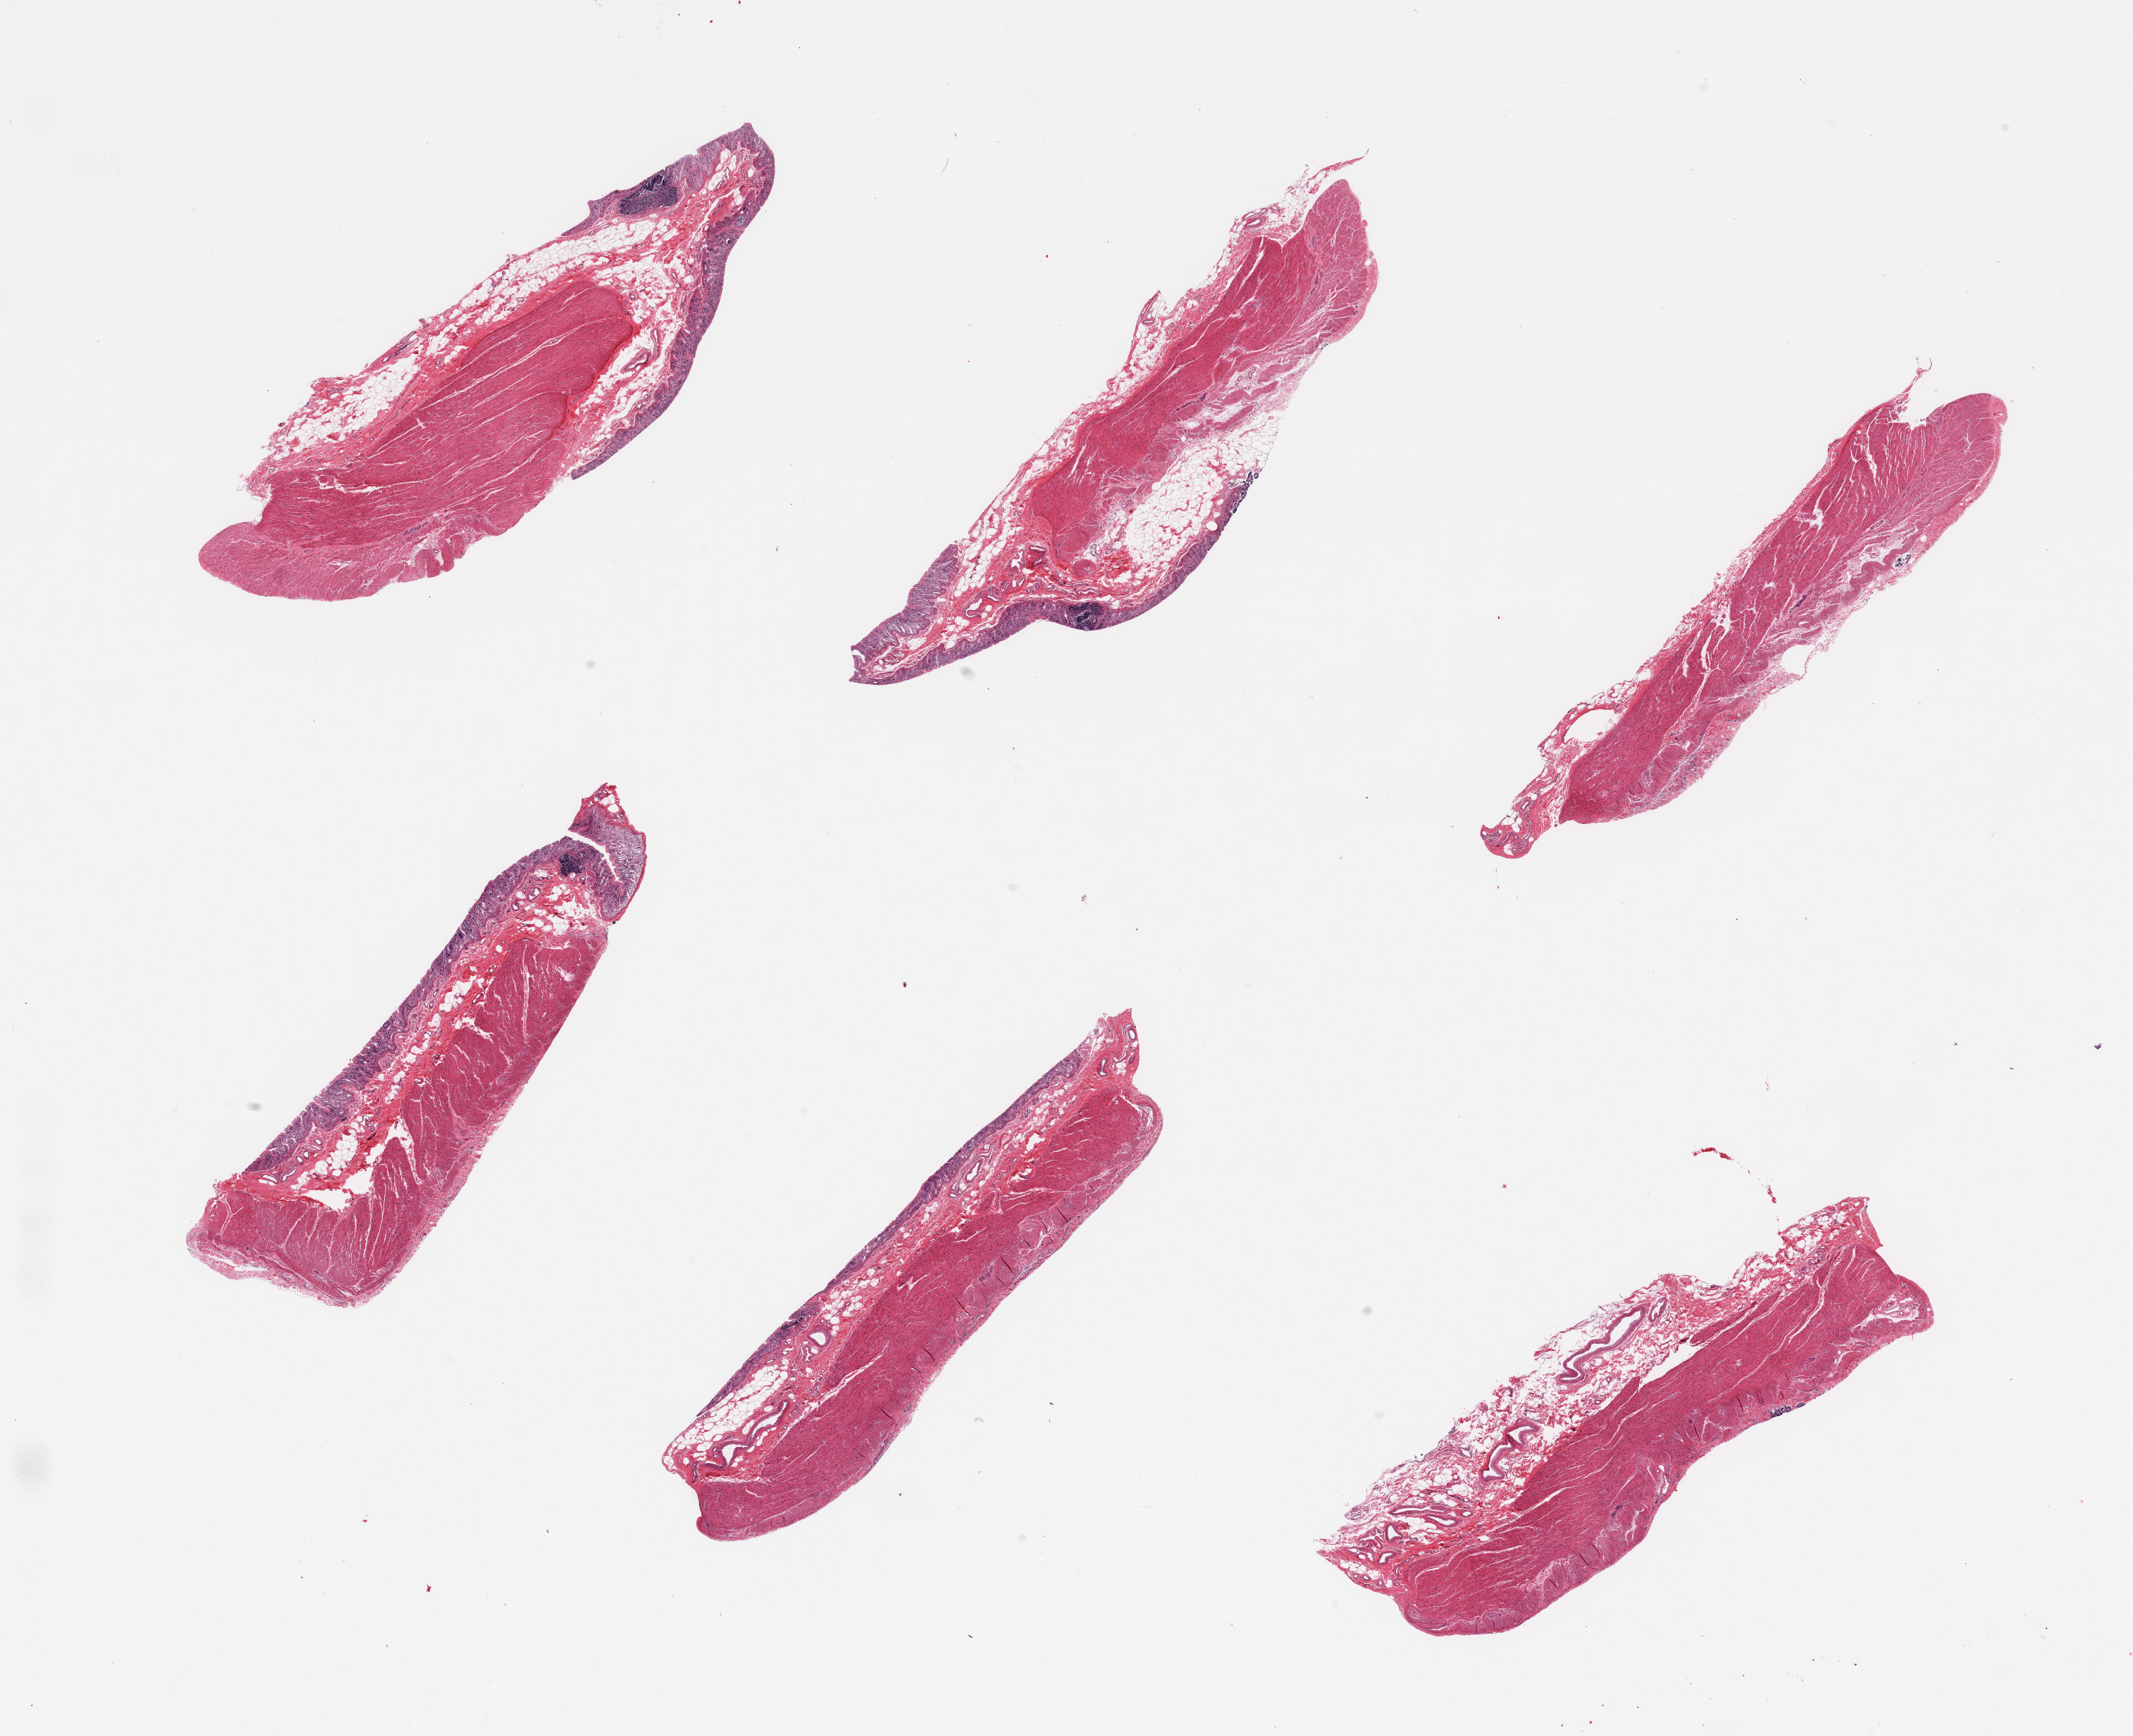
Whole-slide image, haematoxylin and eosin stain, brightfield, shown as a low-resolution overview of the whole scanned area (about 23.6 x 19.2 mm). PAXgene-fixed paraffin-embedded (PFPE) section. Section of transverse colon (target tissue). Donor tissue sample. Donor: male.
Review note (as recorded): 6 pieces; mucosa autolyzed, muscle intact.